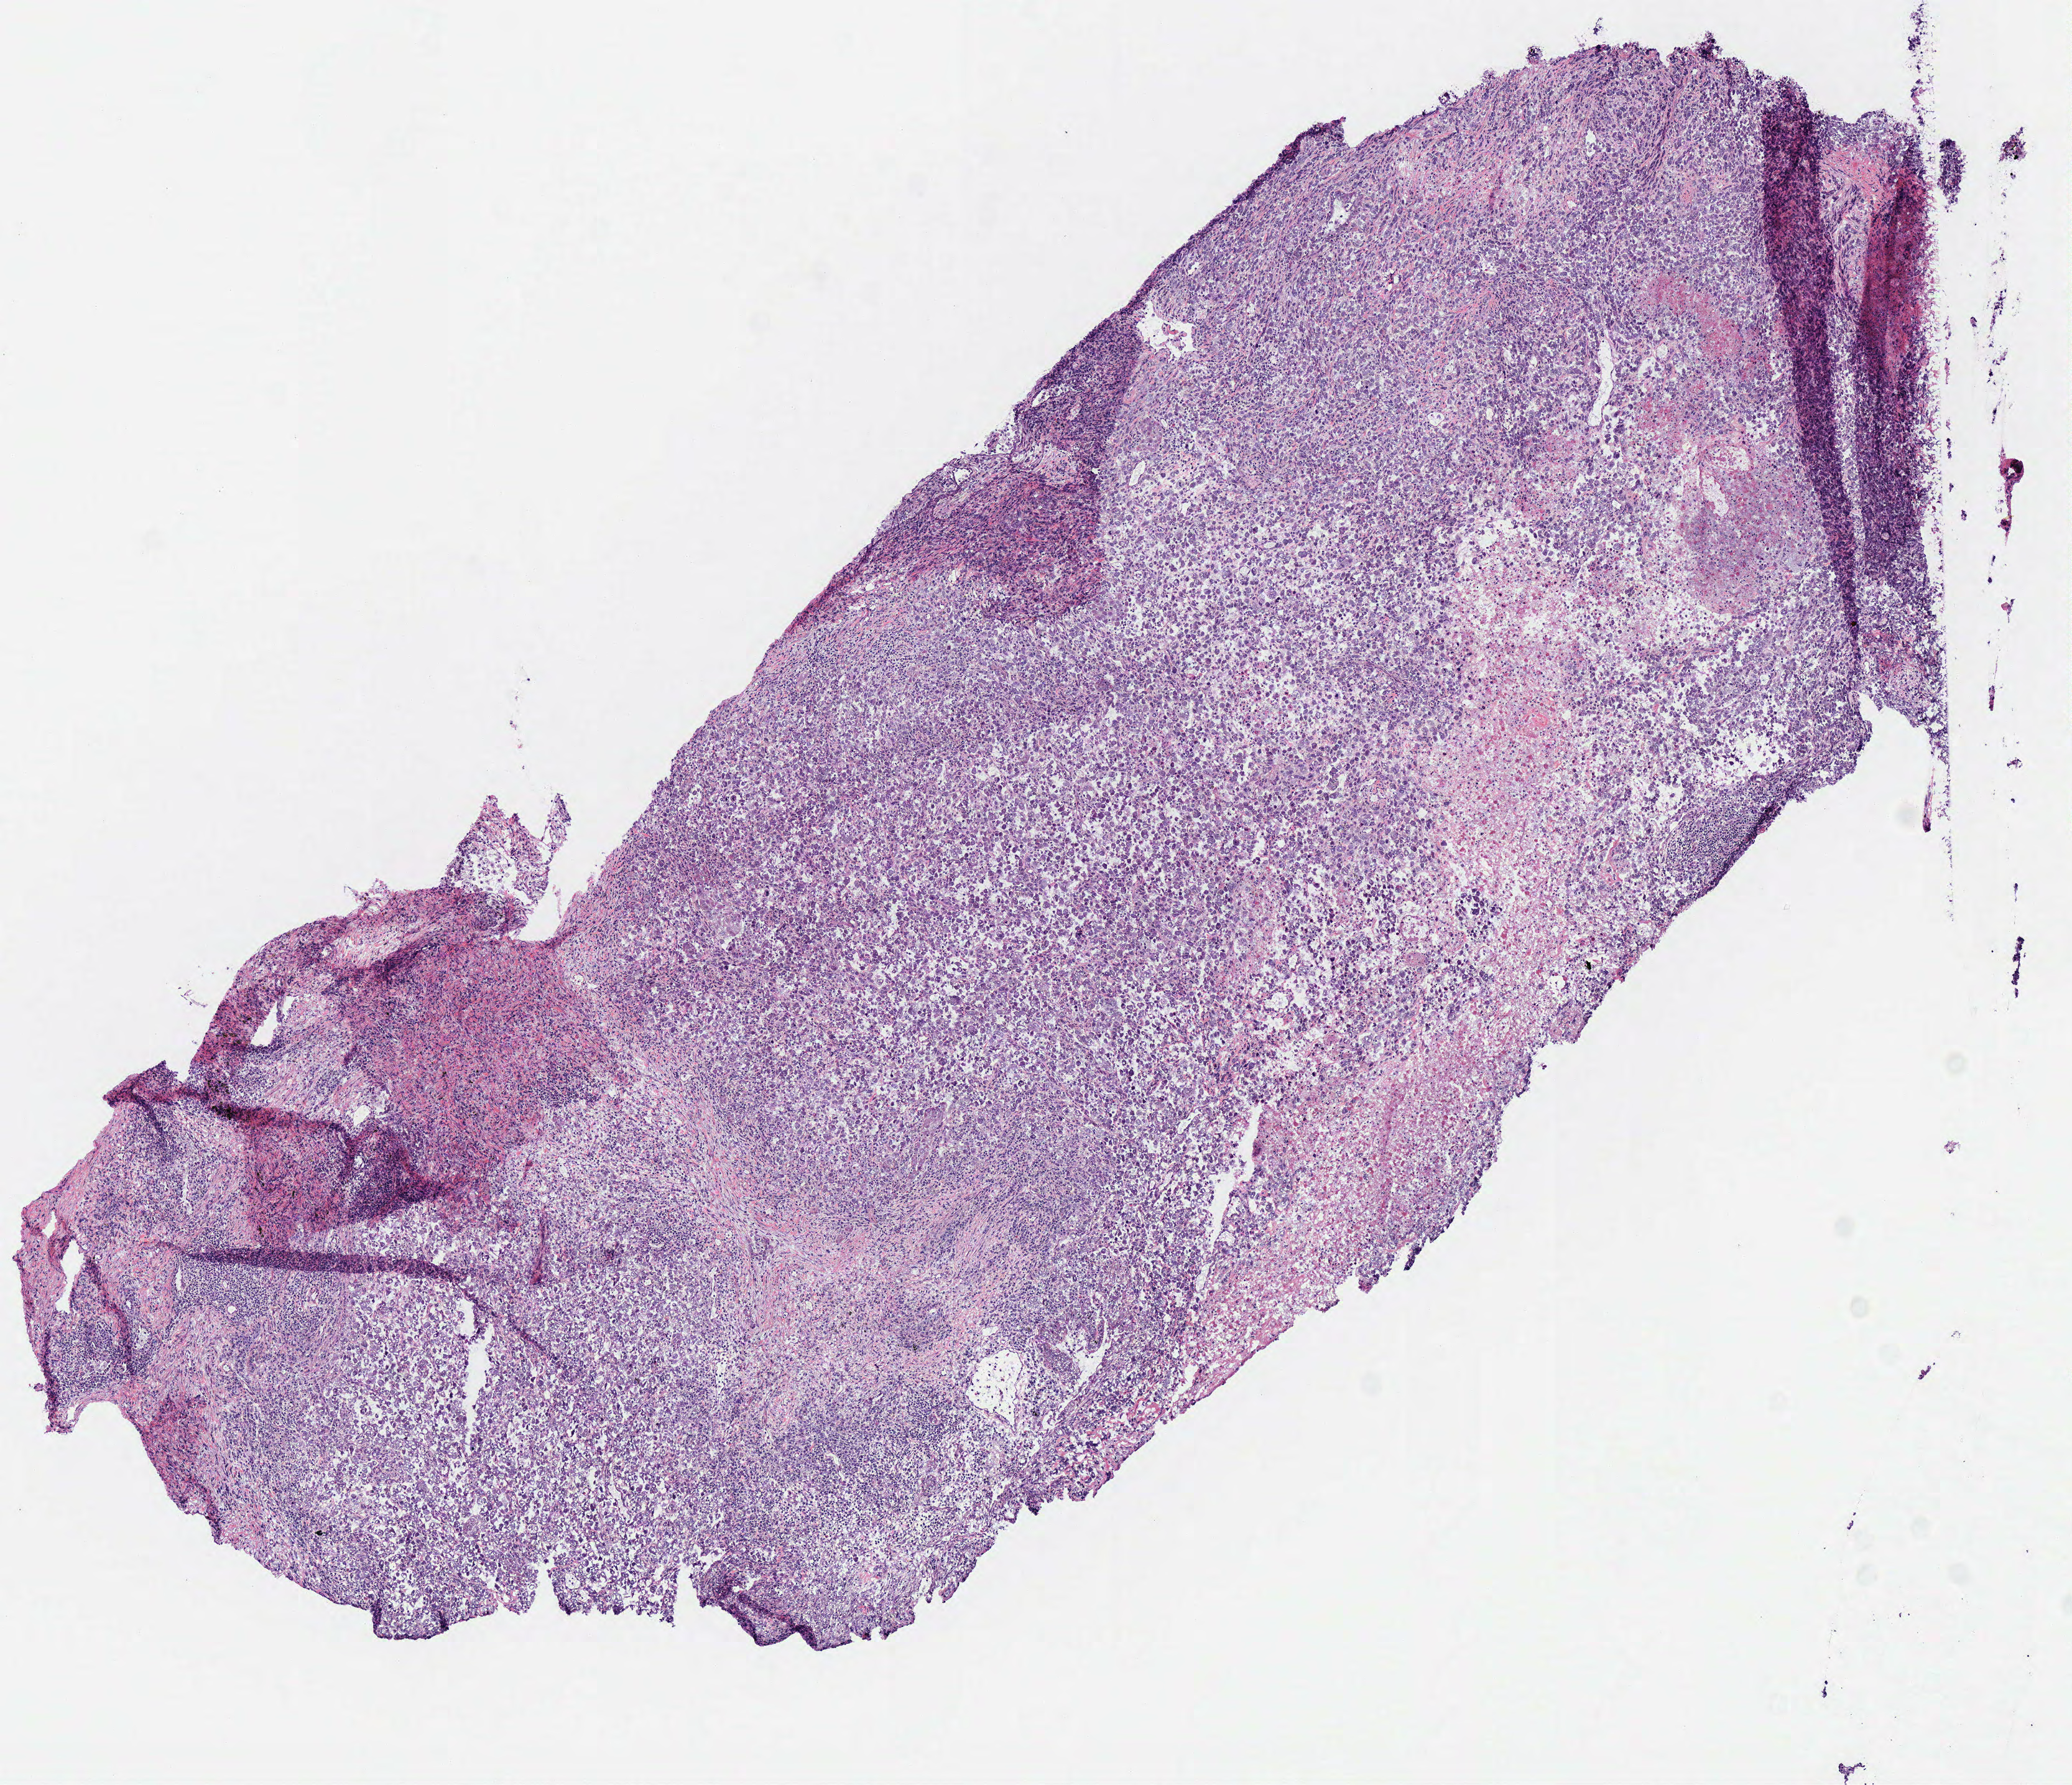
Digitized Hematoxylin and eosin (H&E) stained tissue section (whole slide), shown as a low-resolution overview of the whole scanned area (about 6.6 x 5.7 mm, from a 40x scan); frozen section from the bottom of the tissue portion; lung, primary tumour sample. Male, age 59 years at initial diagnosis. Pathologist review of this section (percent, as recorded): tumour cells 85%, tumour nuclei 80%, normal cells 0%, stromal cells 5%, necrosis 10%.
Laterality: left. AJCC pathologic stage: IIIA (6th edition). Histologic diagnosis: Adenocarcinoma, NOS (upper lobe, lung). TNM: T2 N2 MX.